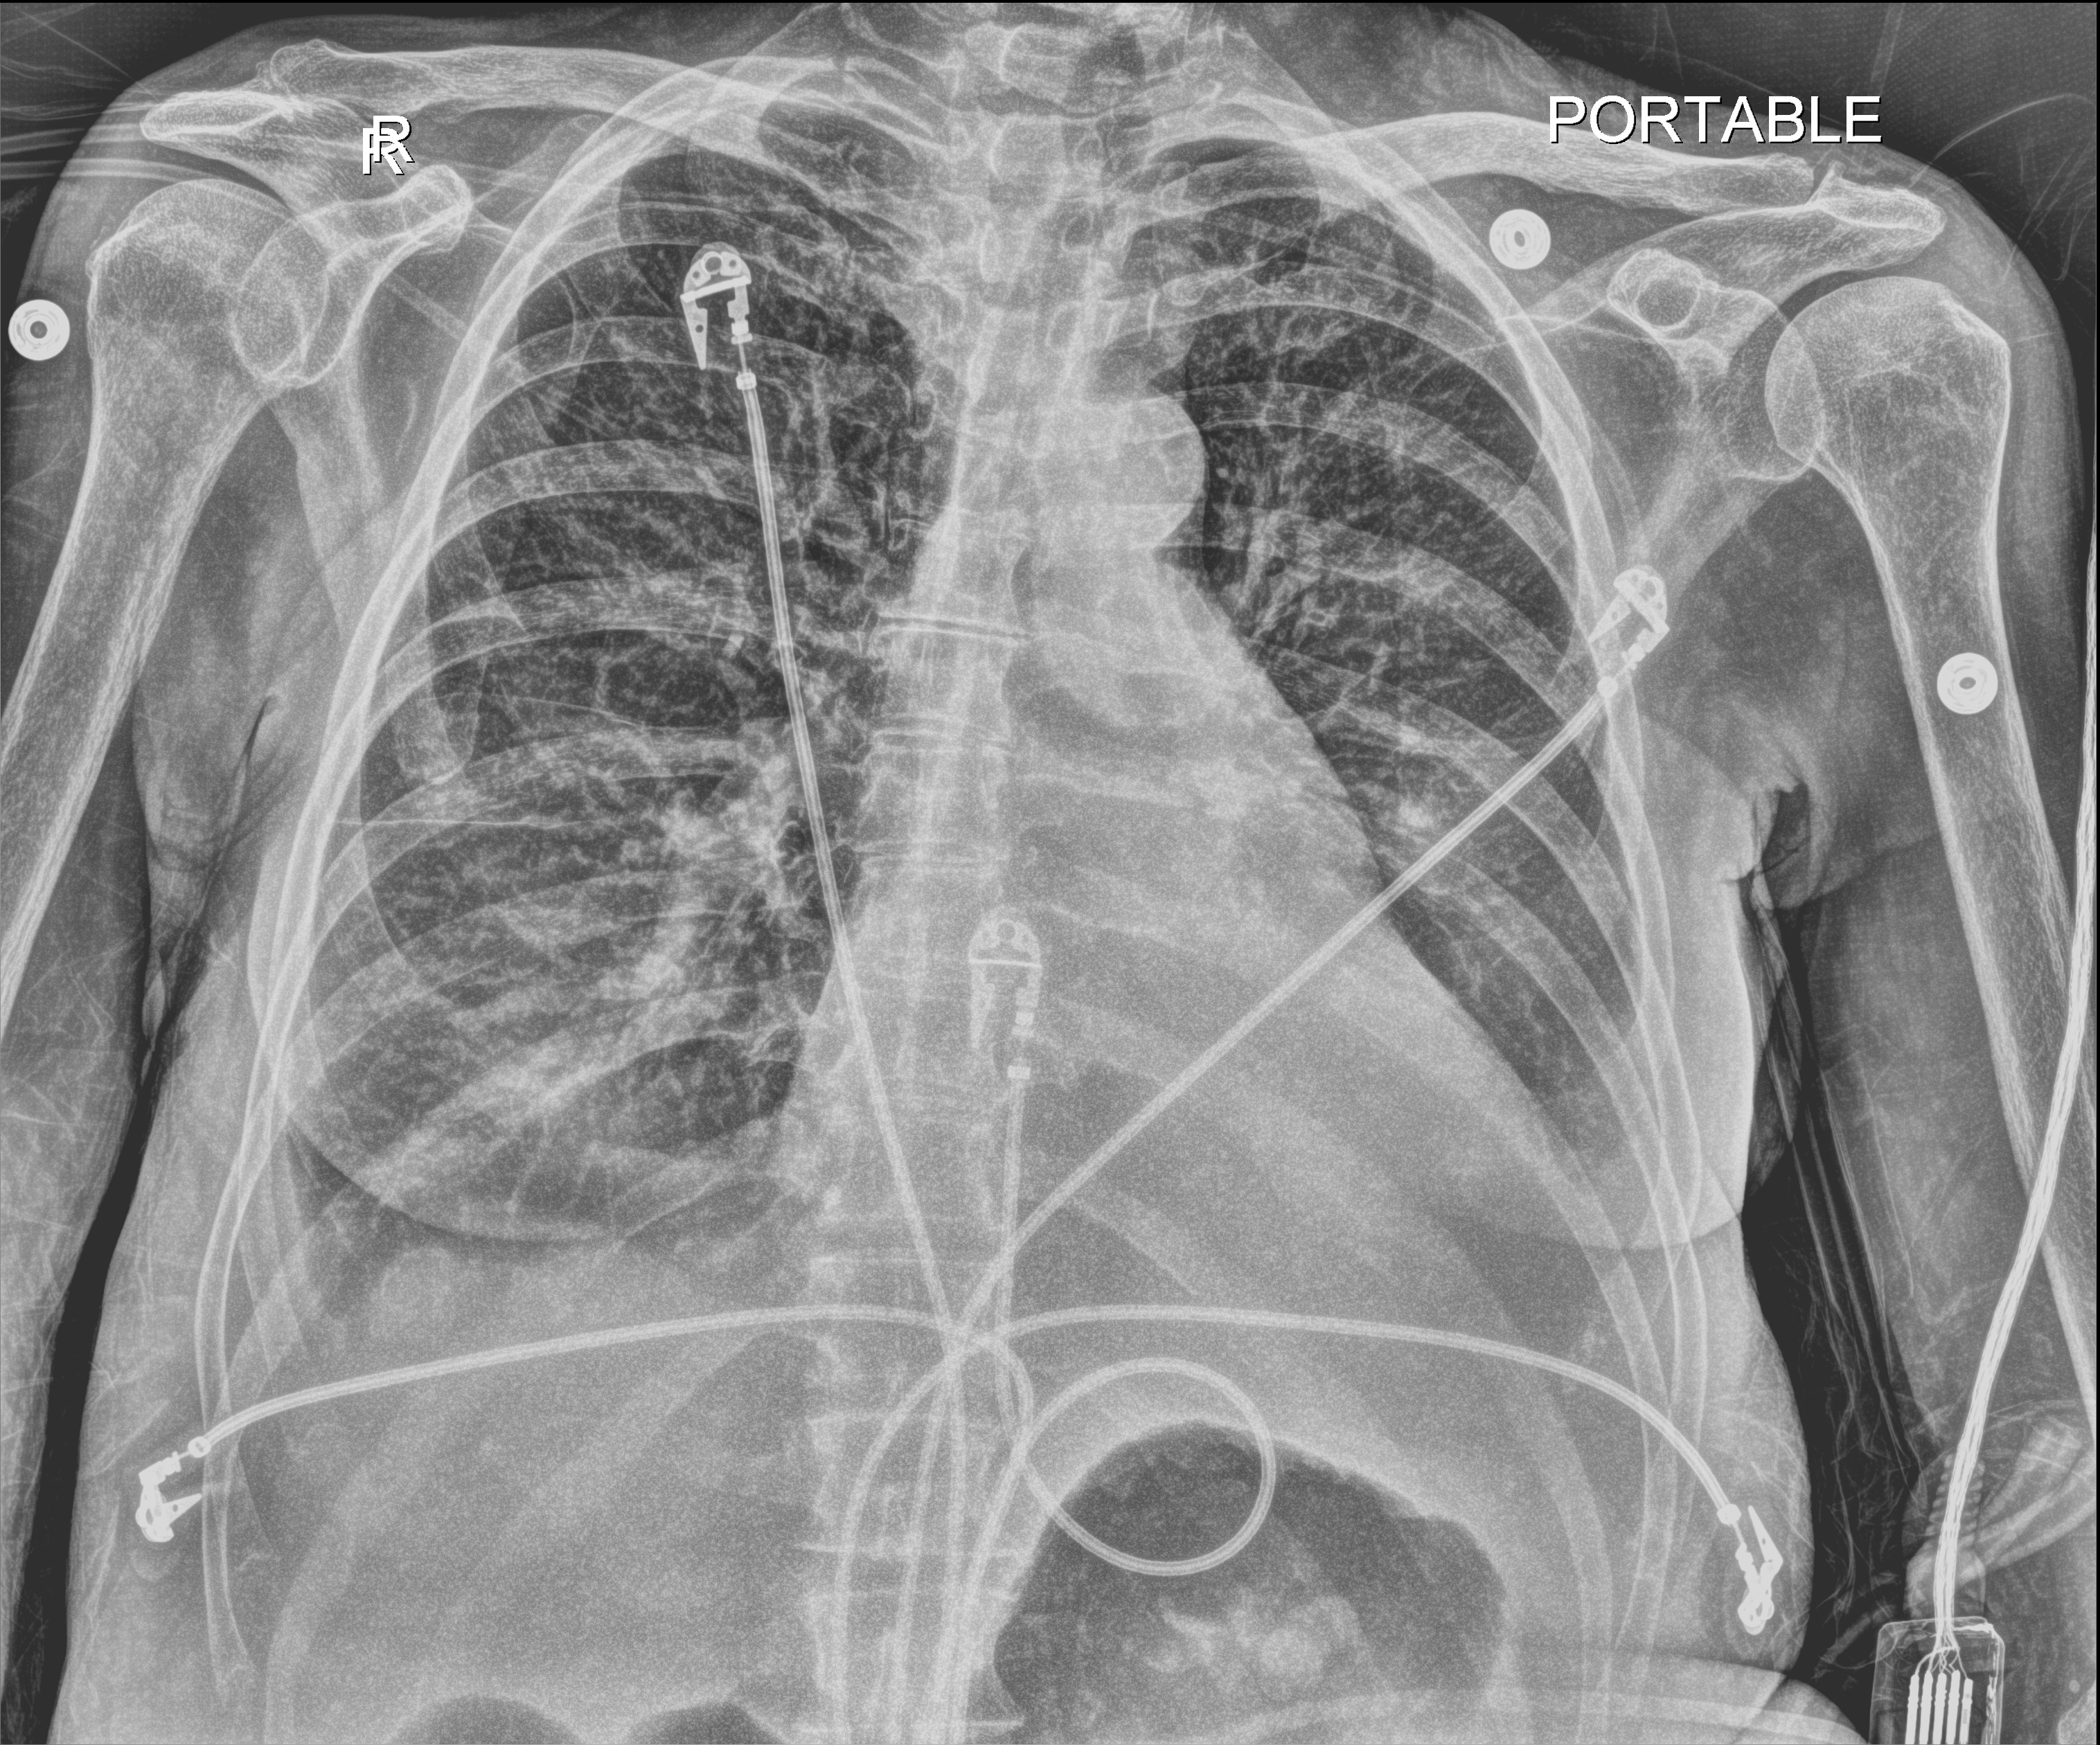
Chest X-ray (portable). Female patient hospitalised with COVID-19, age 60–74 years.
Admission-level facts for this patient (not findings on this image; timing relative to this image not recorded): mechanically ventilated during this hospital stay: yes; length of hospital stay: 38 days.